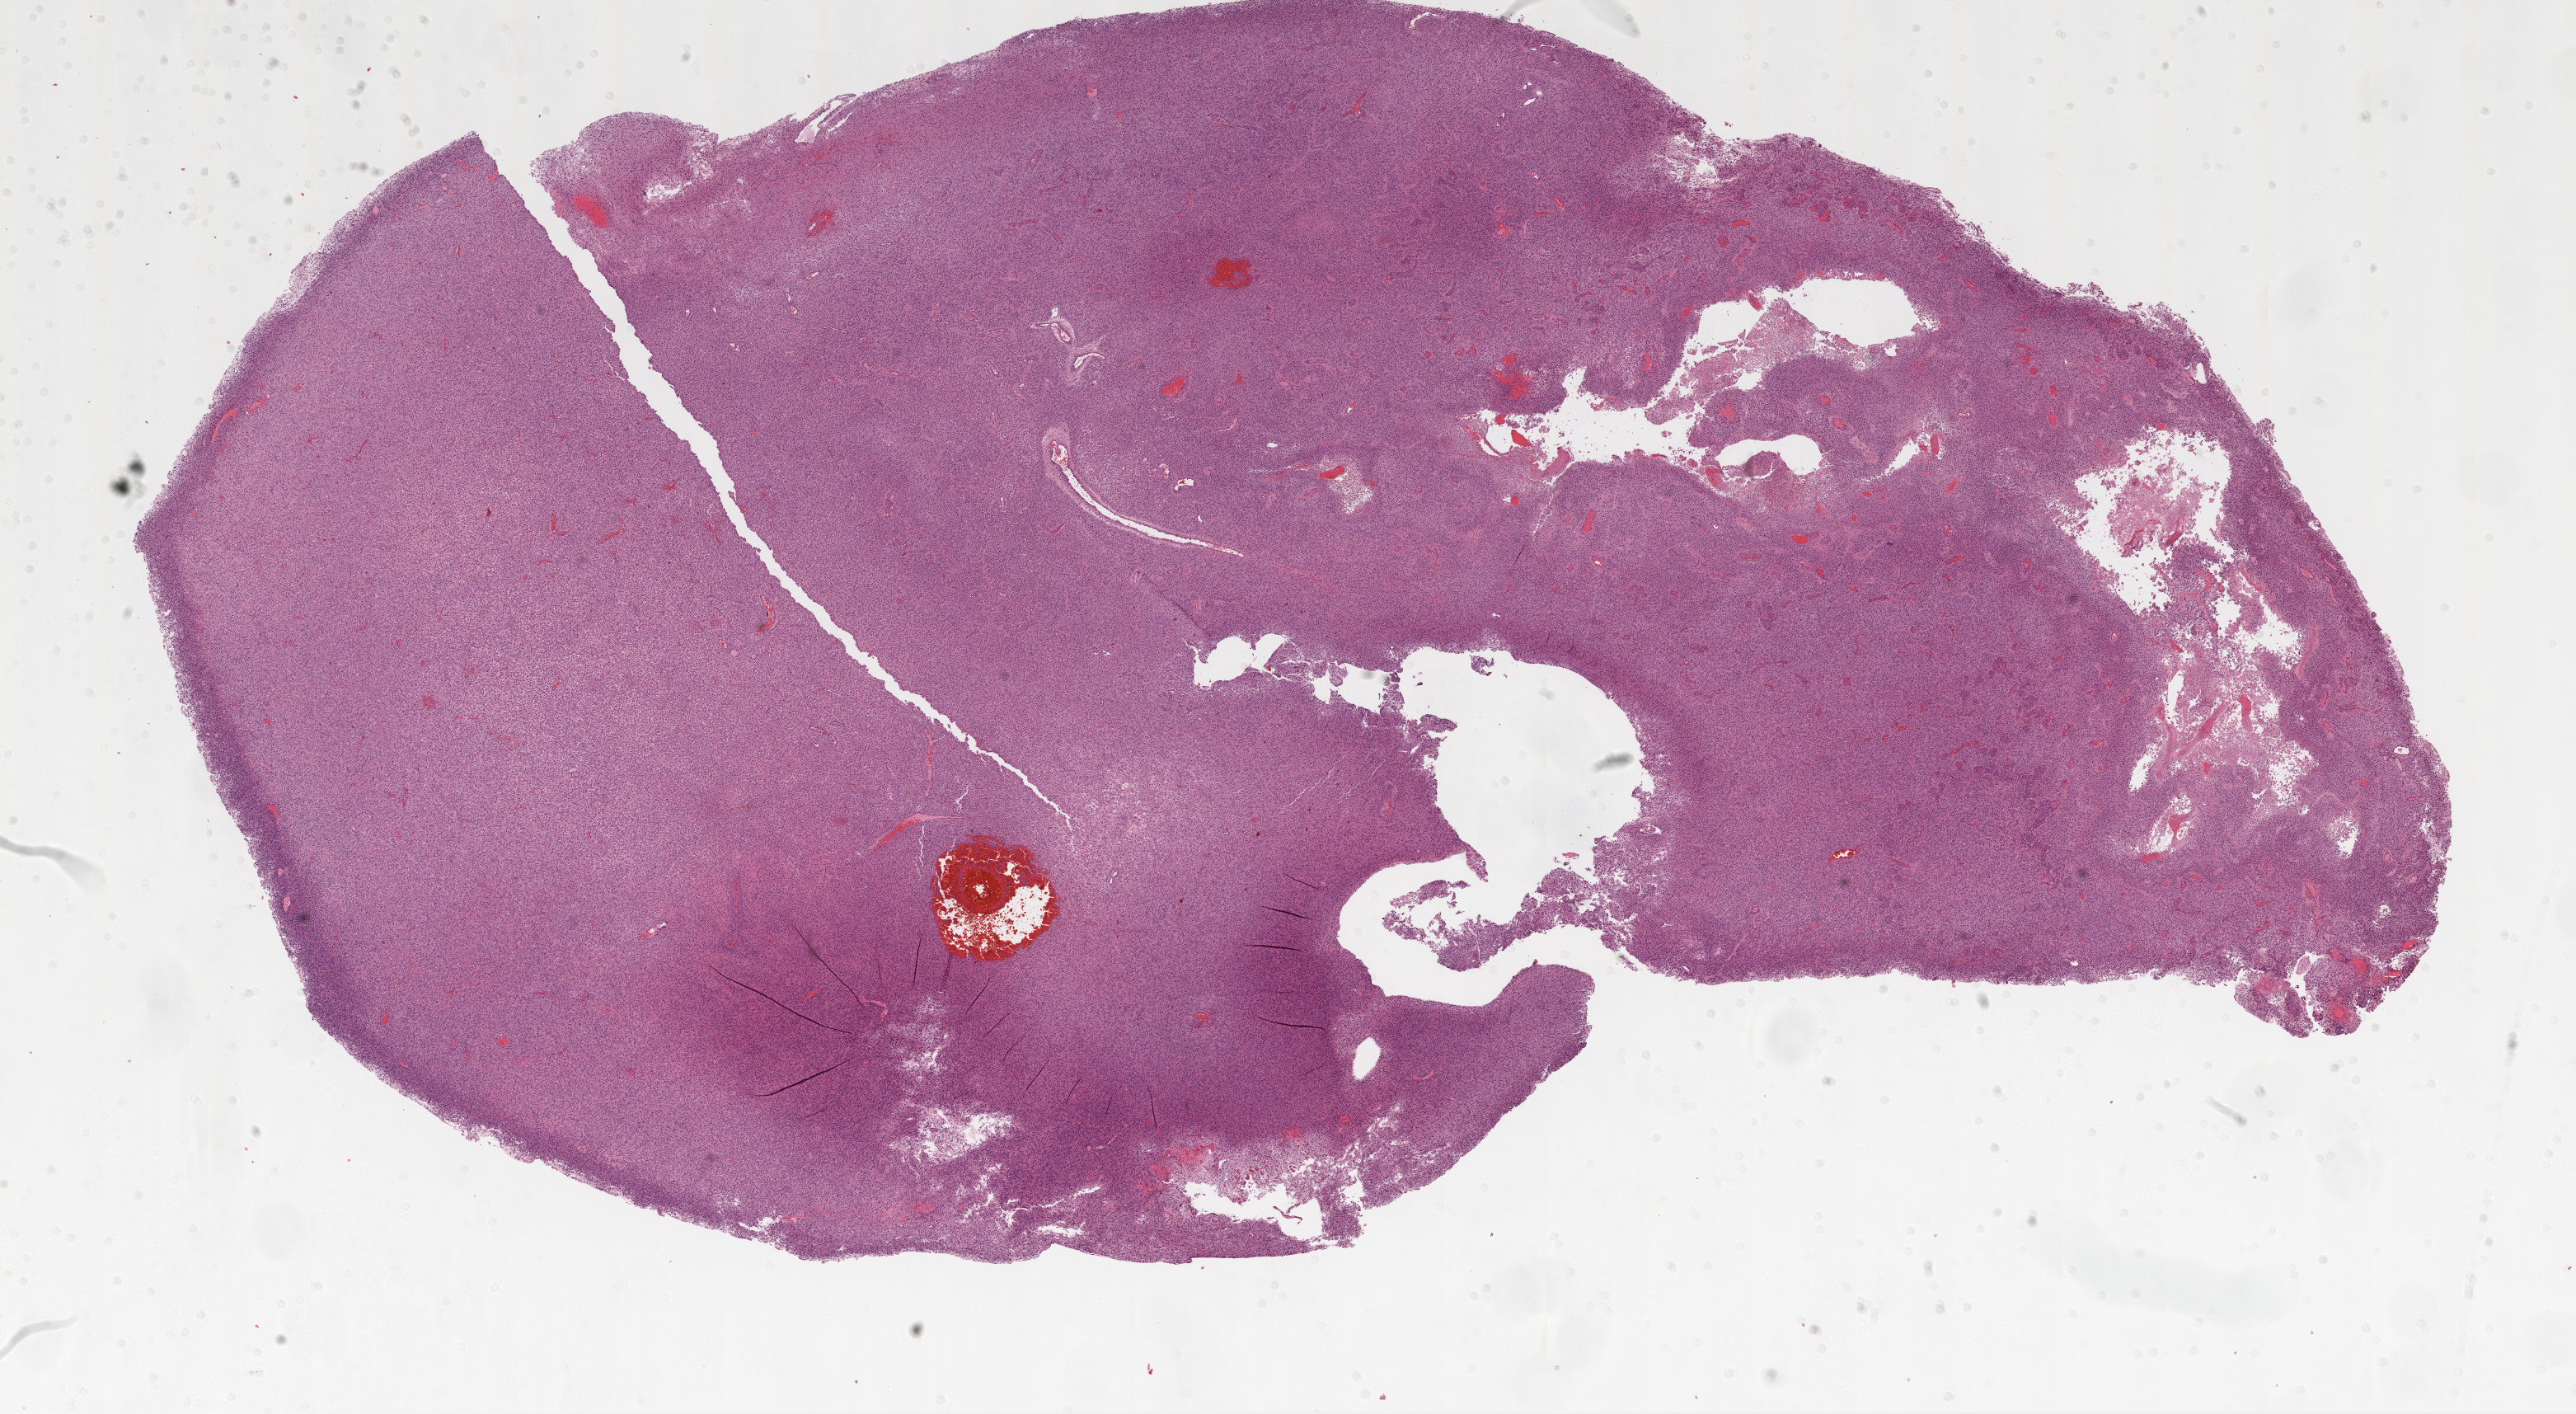
H&E whole-slide image, a low-resolution overview of the entire scanned area, about 25.1 x 13.8 mm, formalin-fixed paraffin-embedded (FFPE) diagnostic section, primary tumour sample from the brain. Male patient; age at initial diagnosis 55 years.
• pathologic diagnosis: Glioblastoma